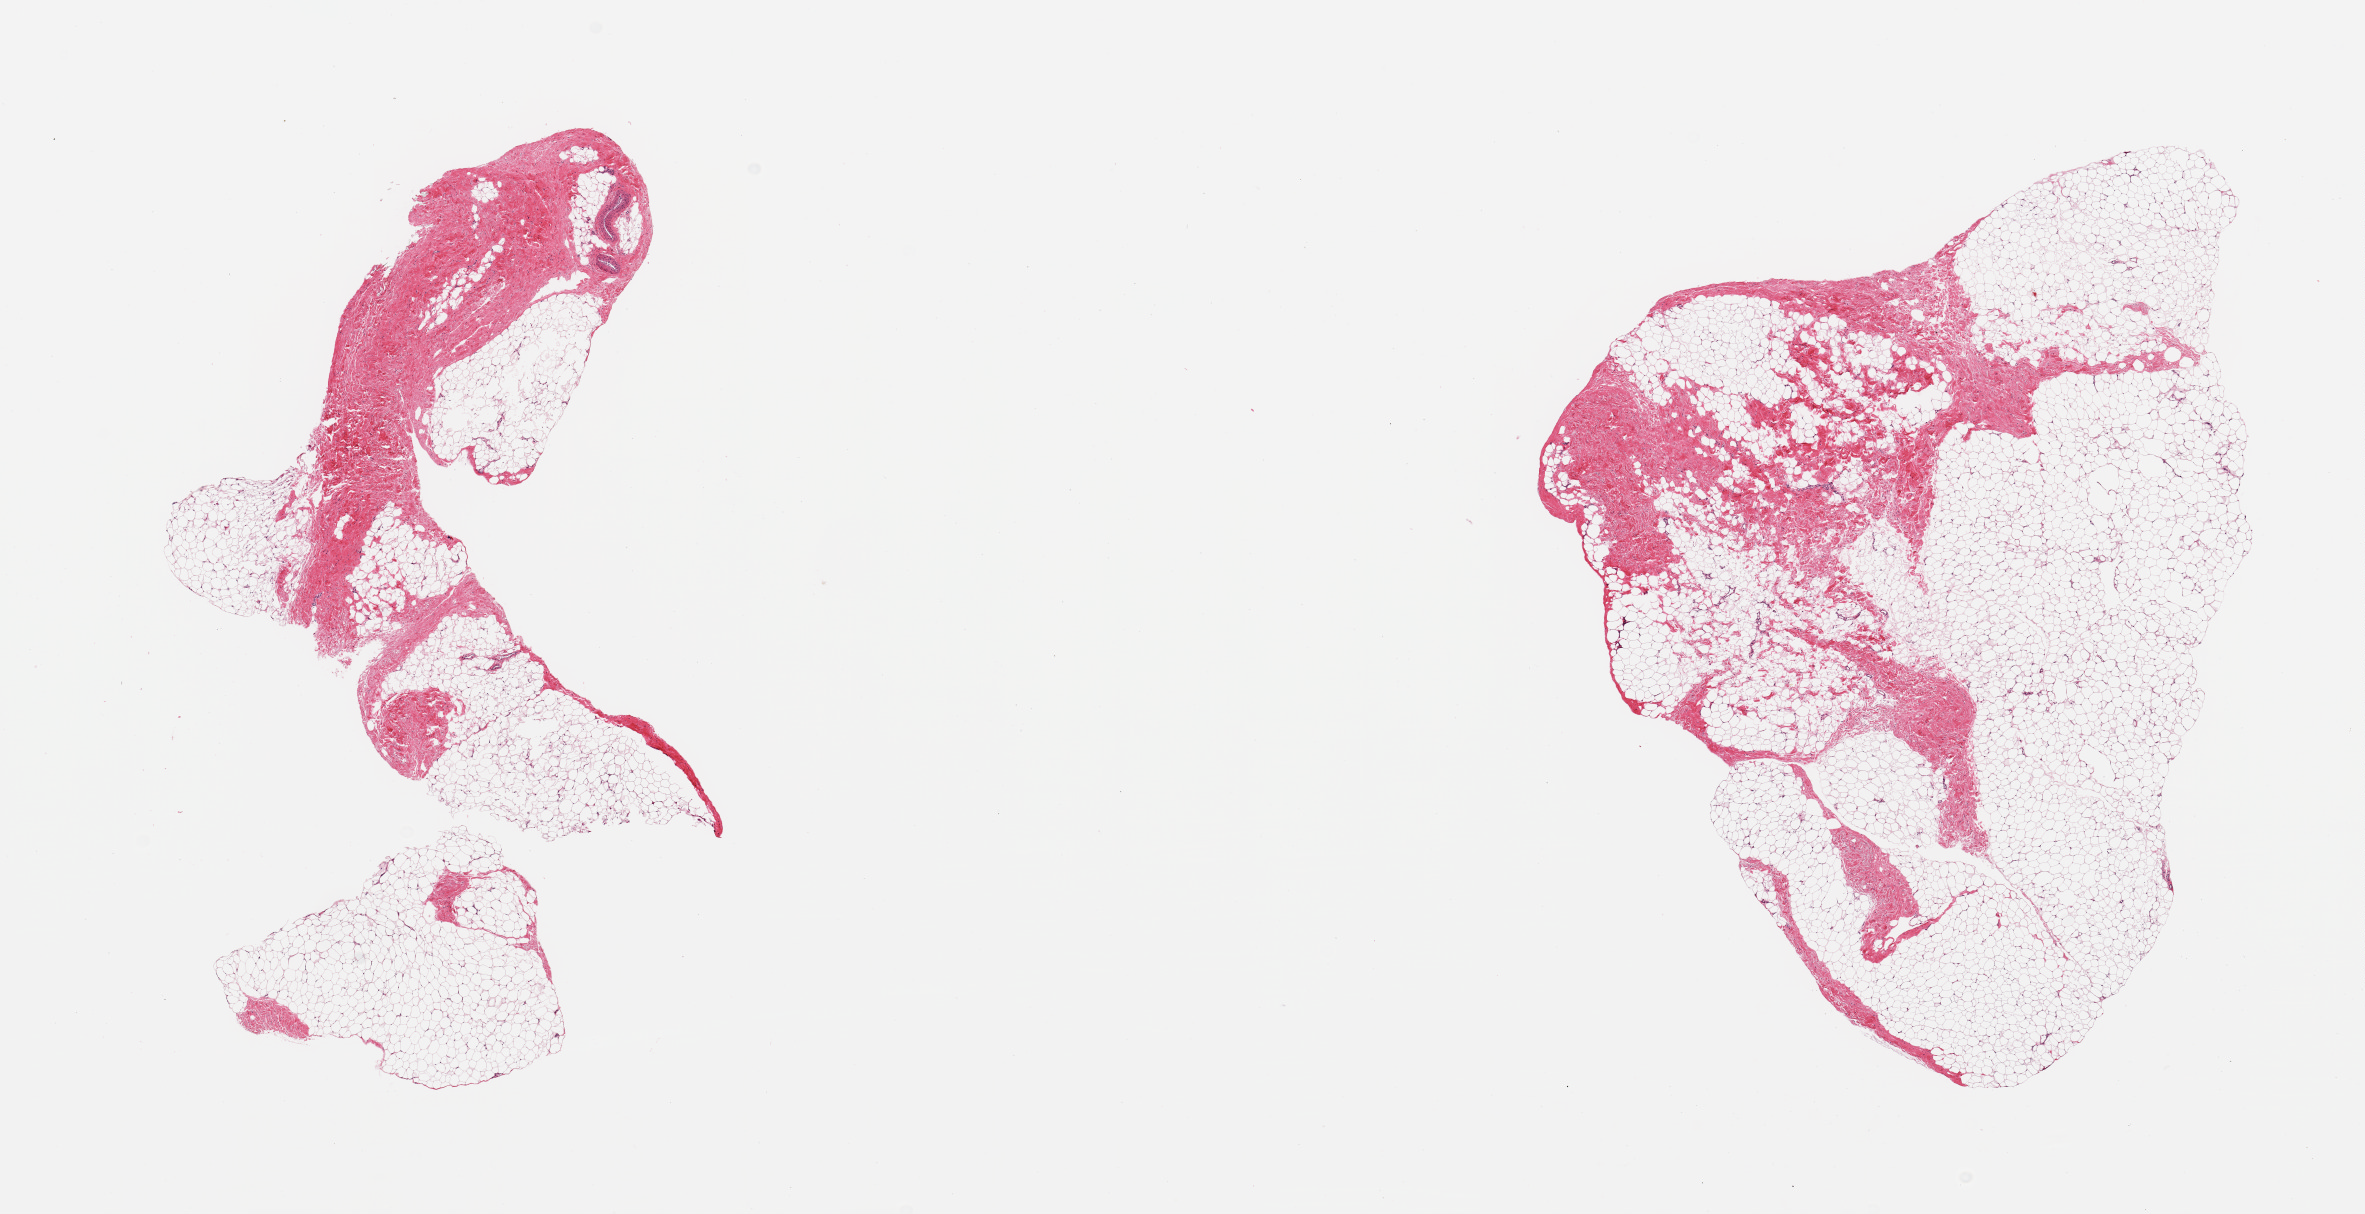
Whole-slide image, hematoxylin and eosin (H&E) stain, whole scanned area (about 18.7 x 9.6 mm) shown as a low-resolution overview. PAXgene-fixed, paraffin-embedded tissue. Section of breast (target tissue). Donor tissue sample. Donor: male.
Reviewer comment on this tissue sample: 2 pieces, fibroadipose elements only, mild gynecomastoid stromal hyperplasia.